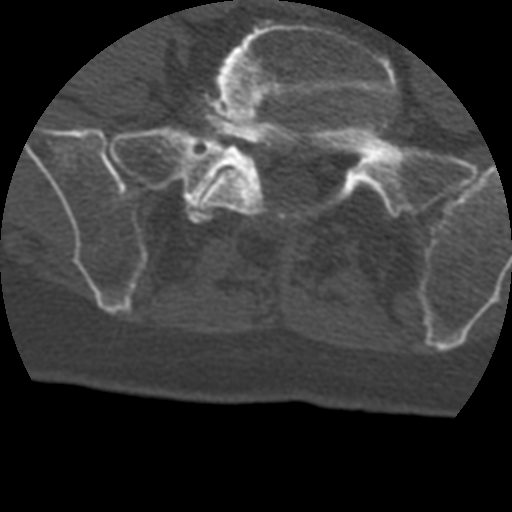
CT including the spine, one axial slice. Slice 33 of 399 in the series (ordered by position). Reconstruction kernel STANDARD. Bone window (W 1800 / L 400 HU). 1.25 mm slice thickness. 512 × 512 image matrix, field of view 160 × 160 mm. Patient age 69 years. Case-level facts recorded for this patient, not image findings: primary cancer: prostate.
Annotated regions visible in this slice (semi-automatic segmentation, software-assisted and operator-edited):
- L5 vertebra: bounding box <198,19,399,215> (left, top, right, bottom; pixels)